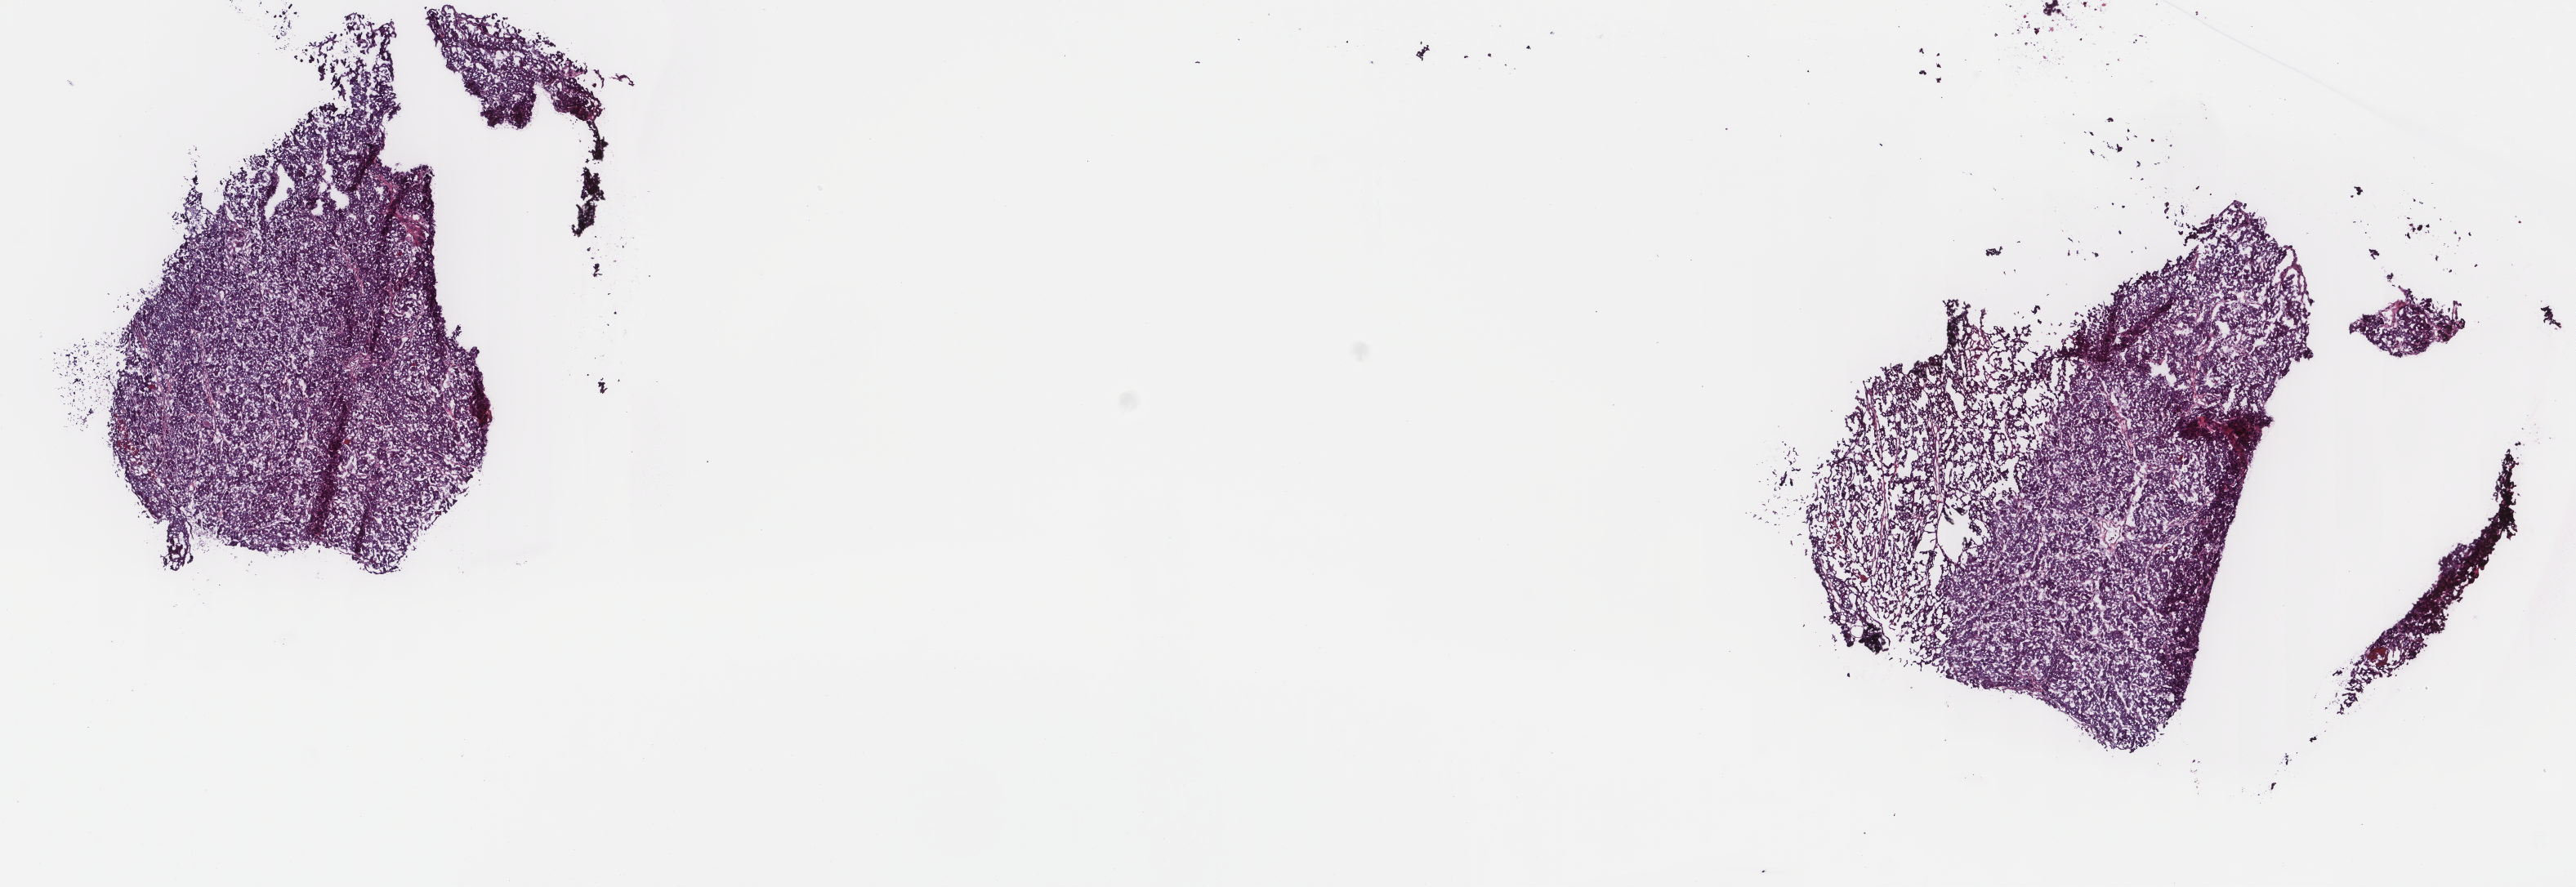
H&E-stained whole-slide image, a low-resolution overview of the entire scanned area, about 12.5 x 4.3 mm (acquisition: 40x scan). Frozen section. Sample: primary tumour, thyroid. Male, age 36 years at initial diagnosis. Slide review estimates, as recorded: tumour cells 95%, tumour nuclei 100%, normal cells 0%, stromal cells 5%, necrosis 0%. Infiltration values recorded for this section: lymphocyte infiltration 1%, monocyte infiltration 3%, neutrophil infiltration 0%.
Diagnosis: Papillary carcinoma, follicular variant (thyroid gland). AJCC pathologic stage: I (7th edition).